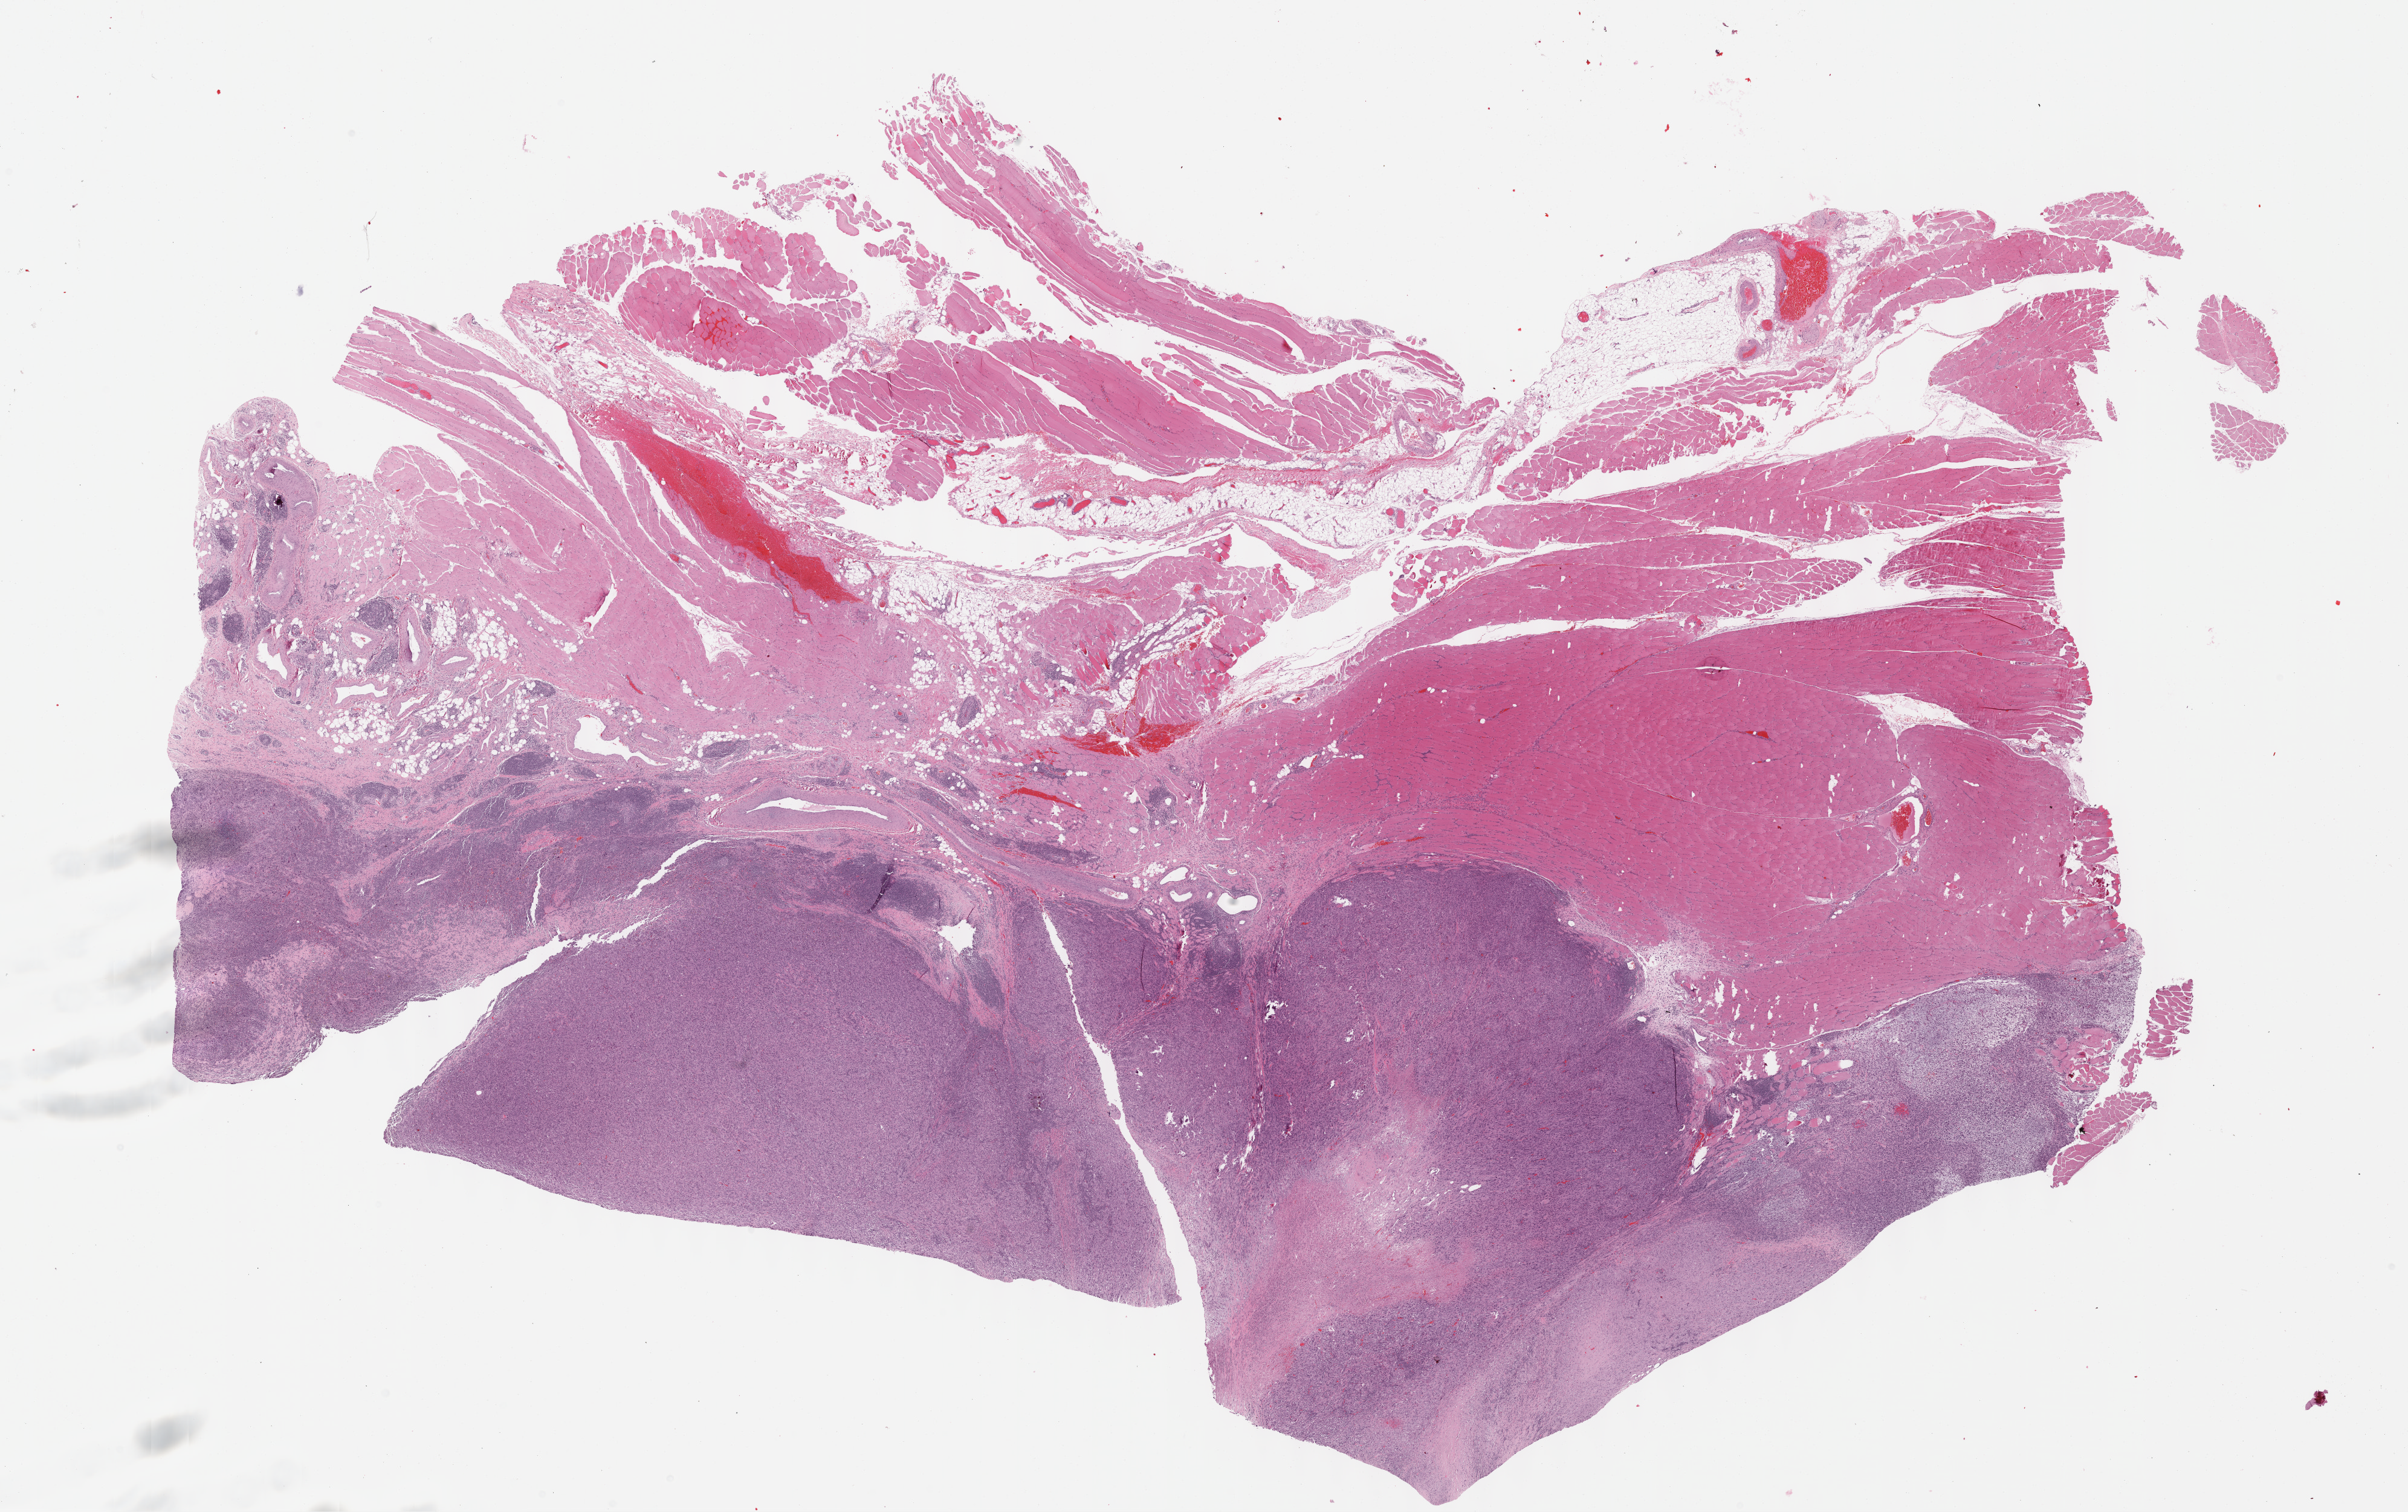
Whole-slide histology image, H&E-stained, low-resolution overview of the scanned area, about 32.2 x 20.2 mm (from a 40x scan). Formalin-fixed paraffin-embedded (FFPE) diagnostic section. Primary tumour sample from the connective, subcutaneous and other soft tissues. Male, age 59 years at initial diagnosis.
Pathologic diagnosis: Undifferentiated sarcoma.